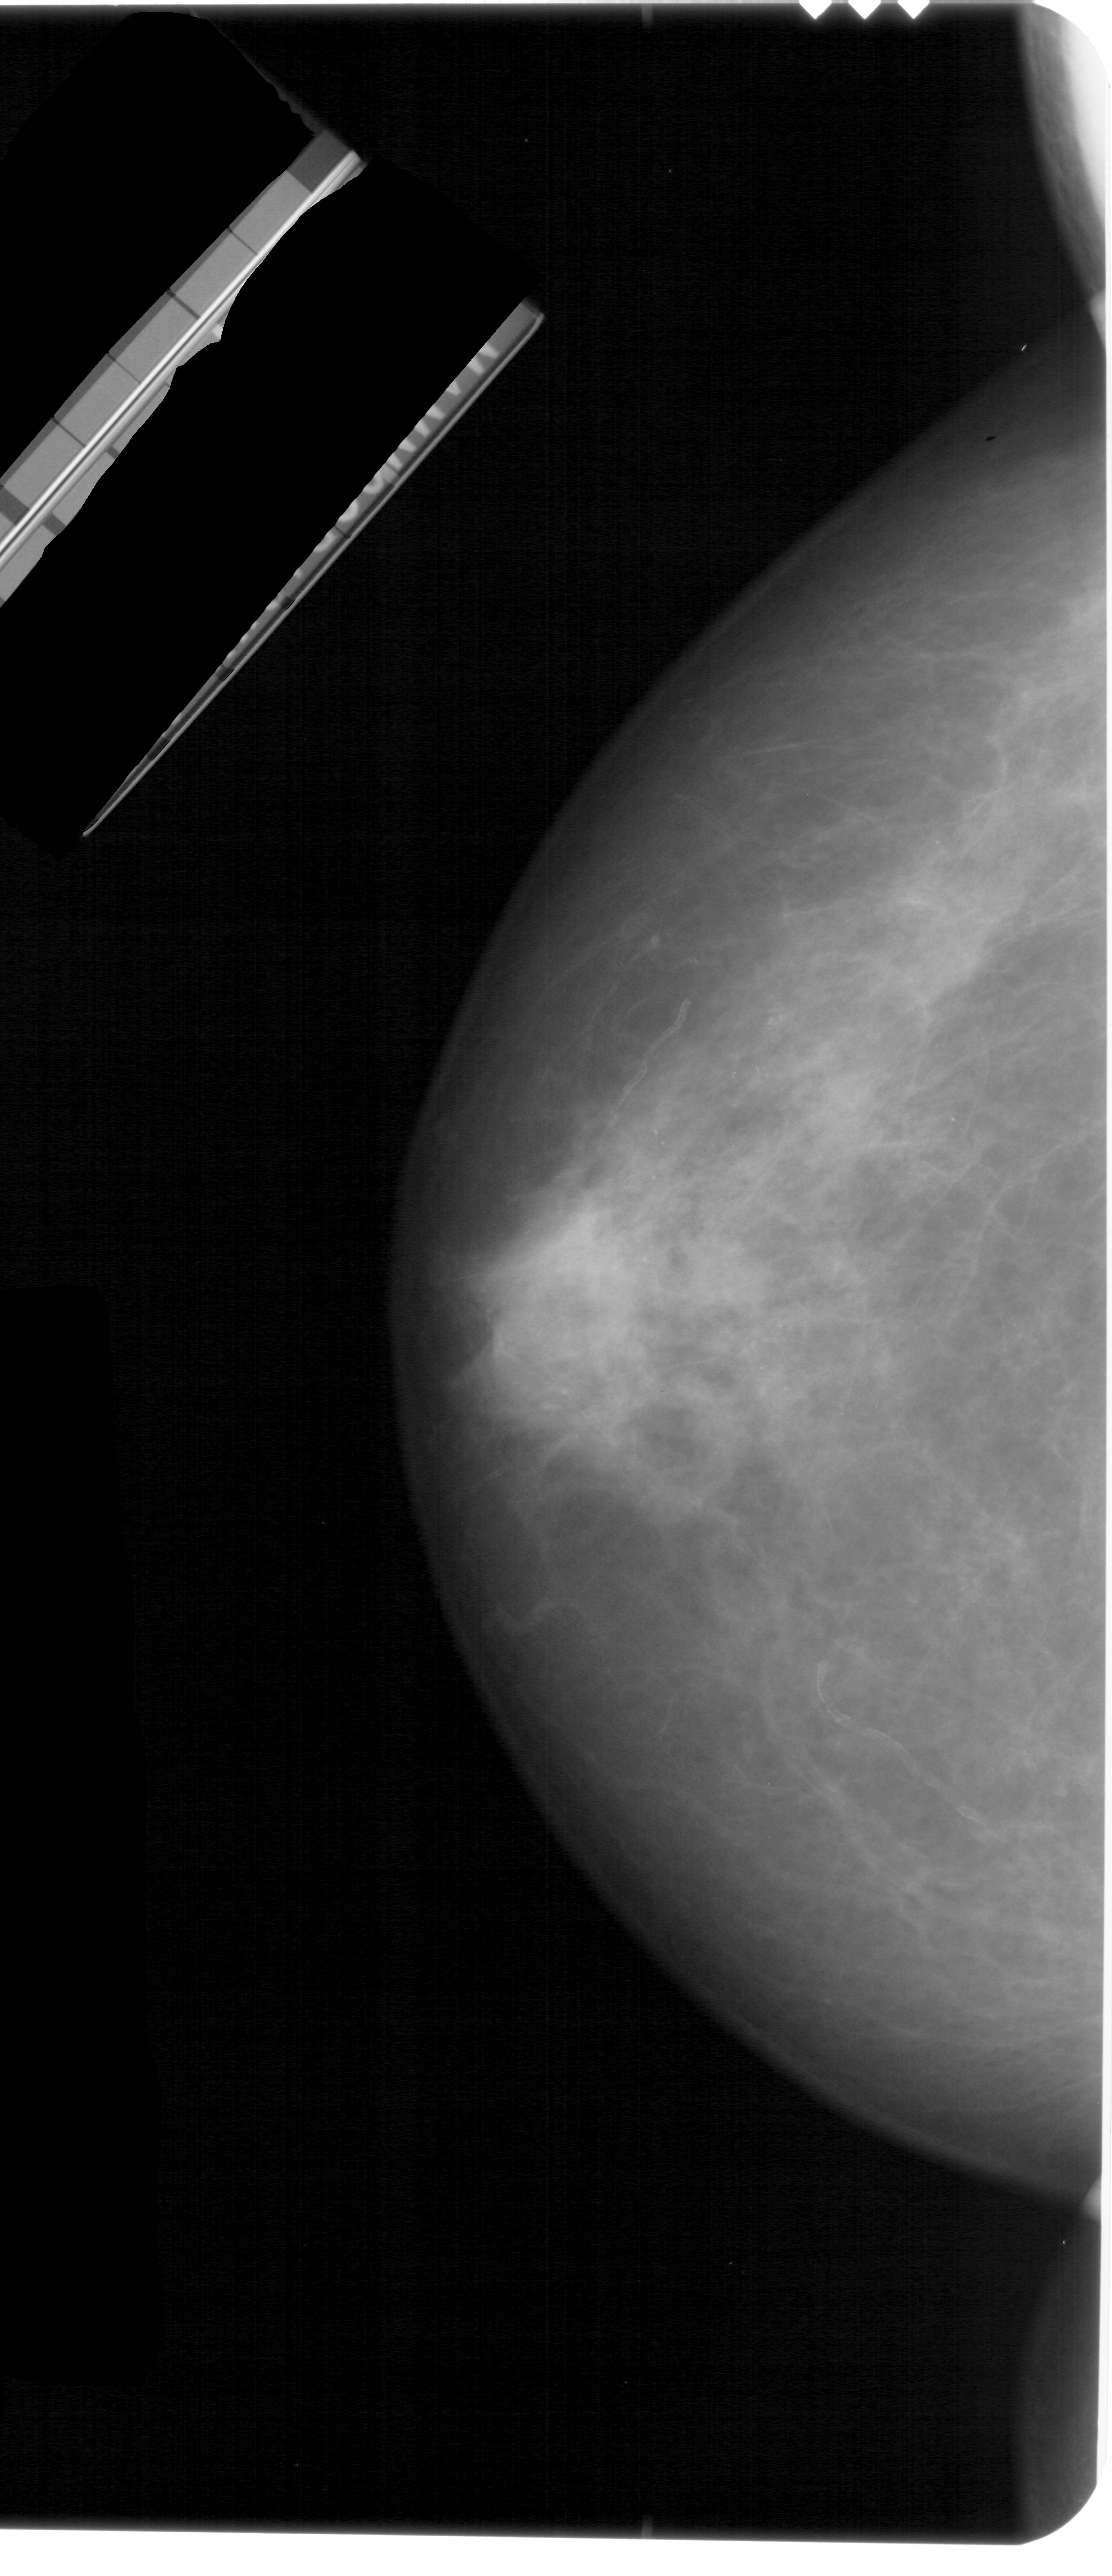
Mammogram (digitized film); left breast; craniocaudal (CC) view; BI-RADS breast density category 4 (scale 1–4).
Radiologist-marked abnormalities on this image: calcifications, morphology punctate / amorphous, distribution regional; BI-RADS assessment category 4; pathology (as recorded): benign.